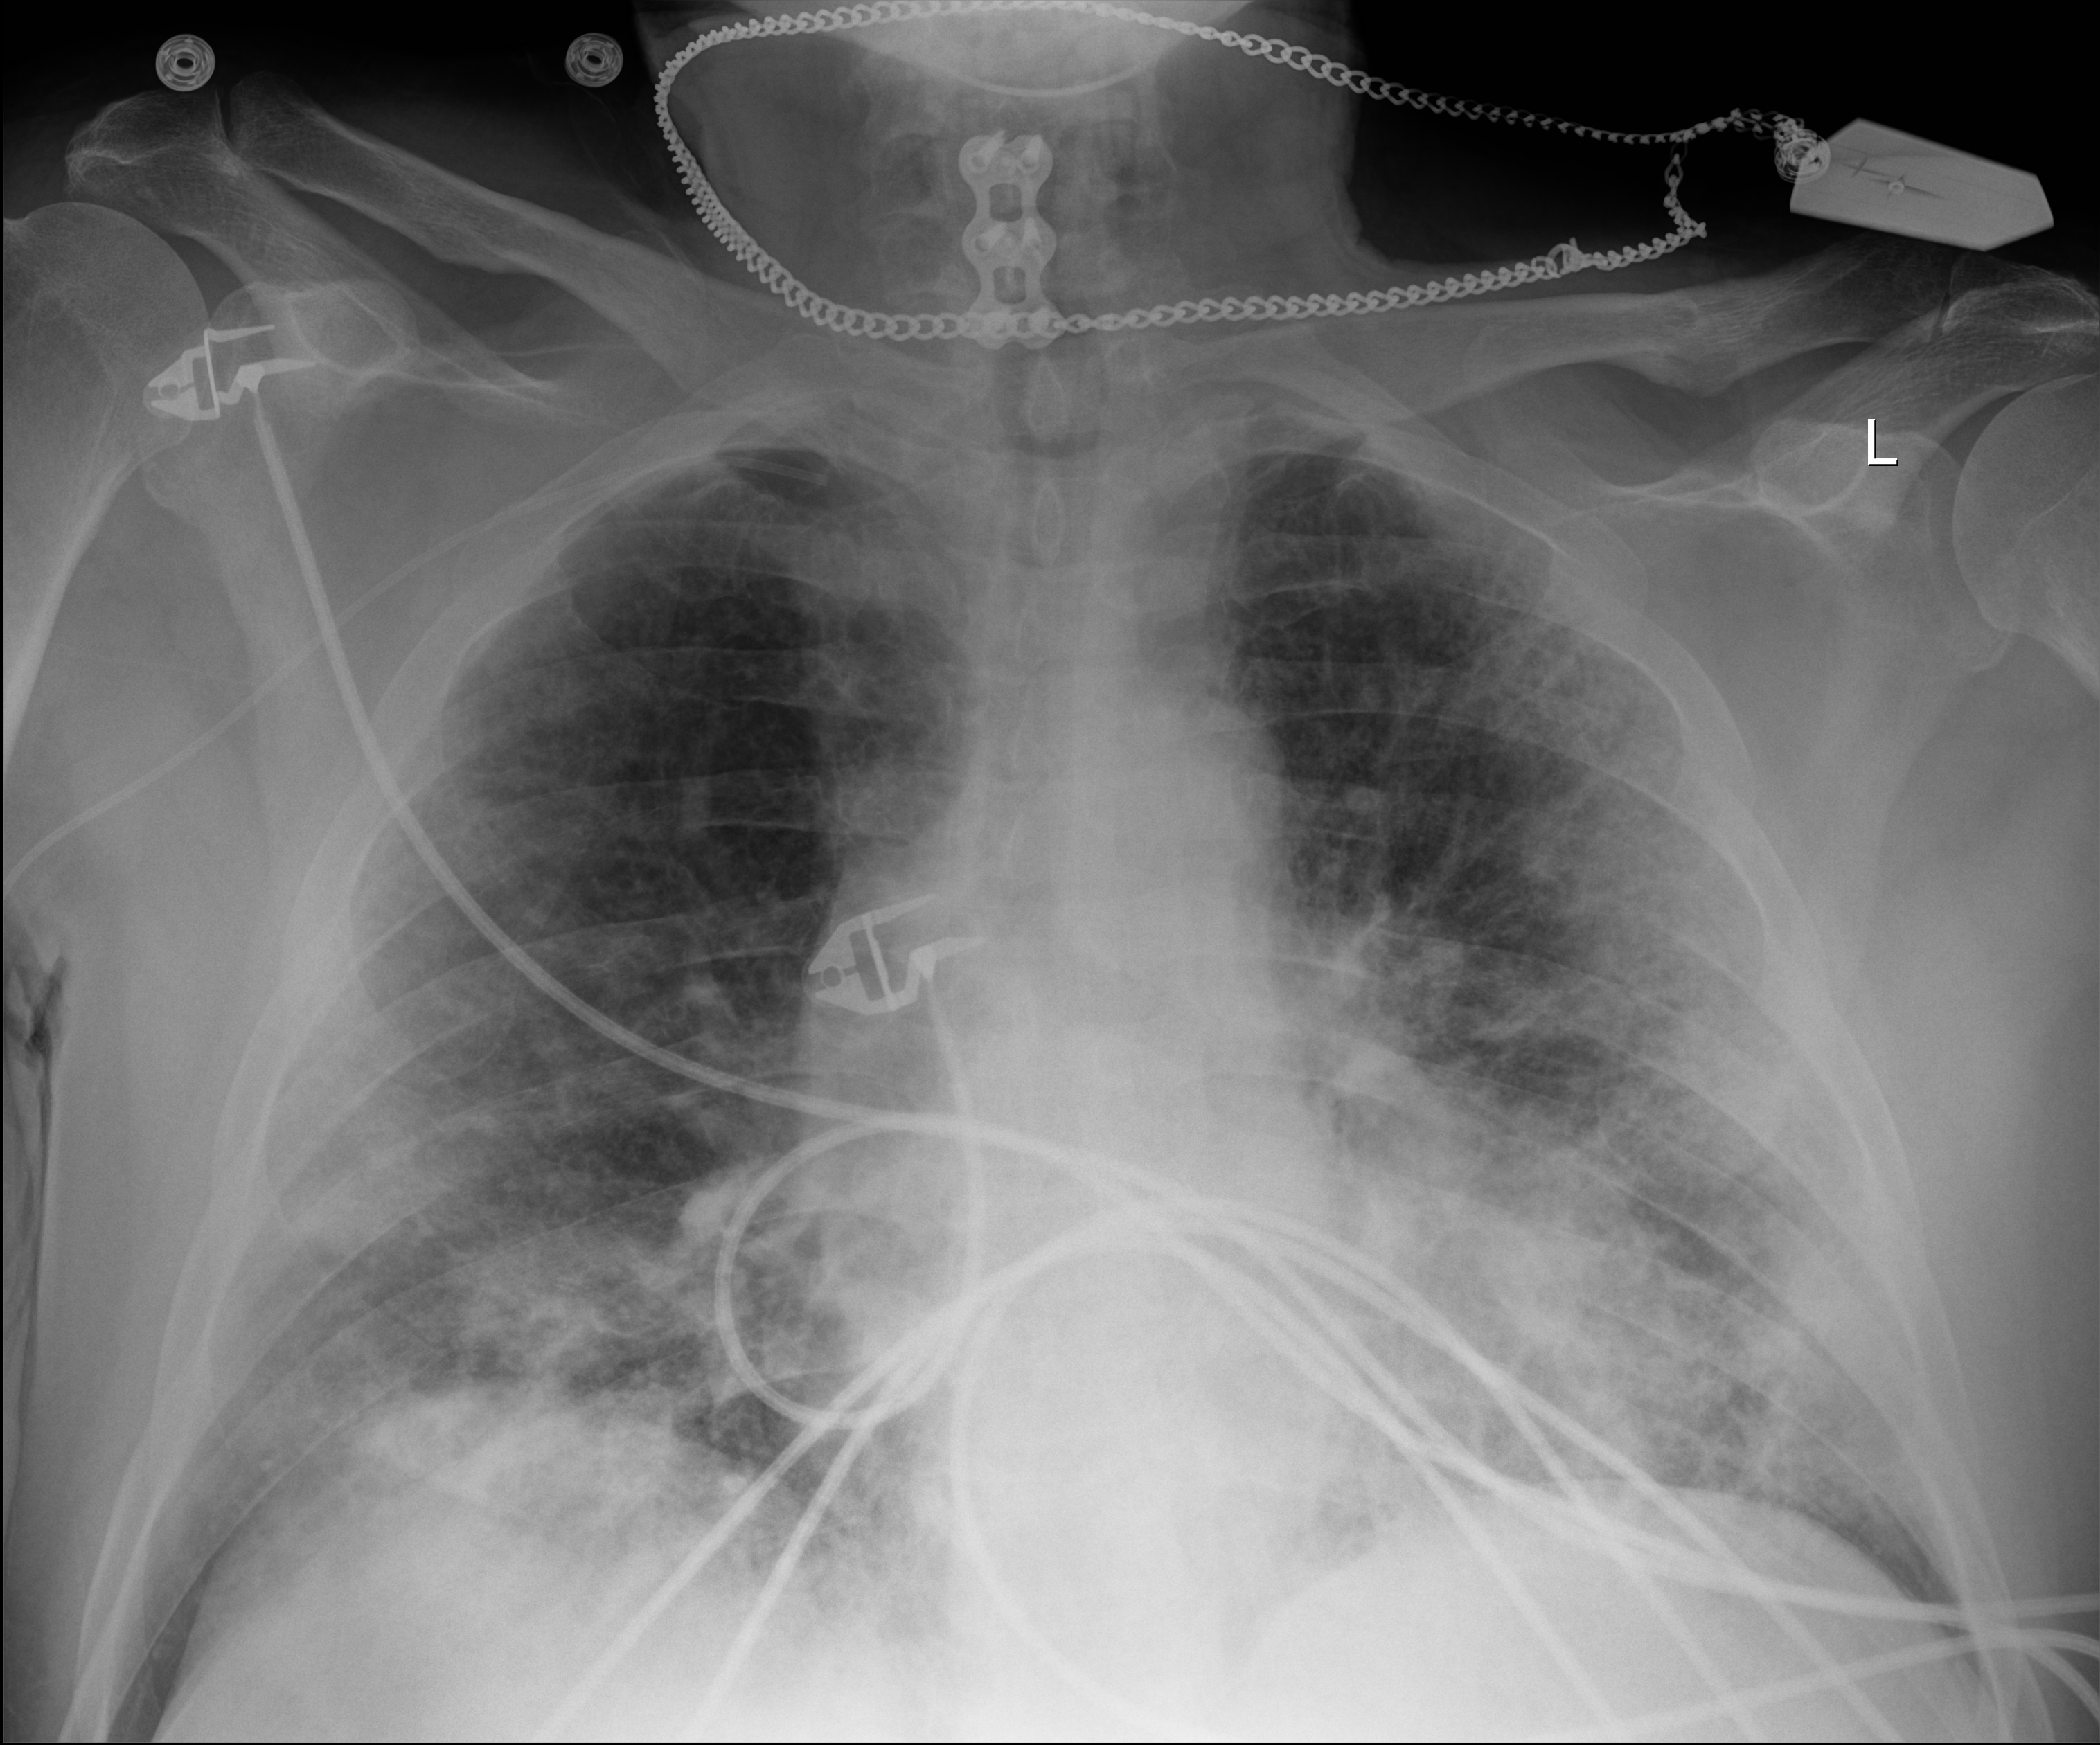
Chest X-ray, anteroposterior (AP) projection. Male patient hospitalised with COVID-19, age 60–74 years.
From the hospital-stay record, not from the radiograph (when in the stay this image was taken is not recorded): mechanically ventilated during this hospital stay: no; diabetes (admission record): no.